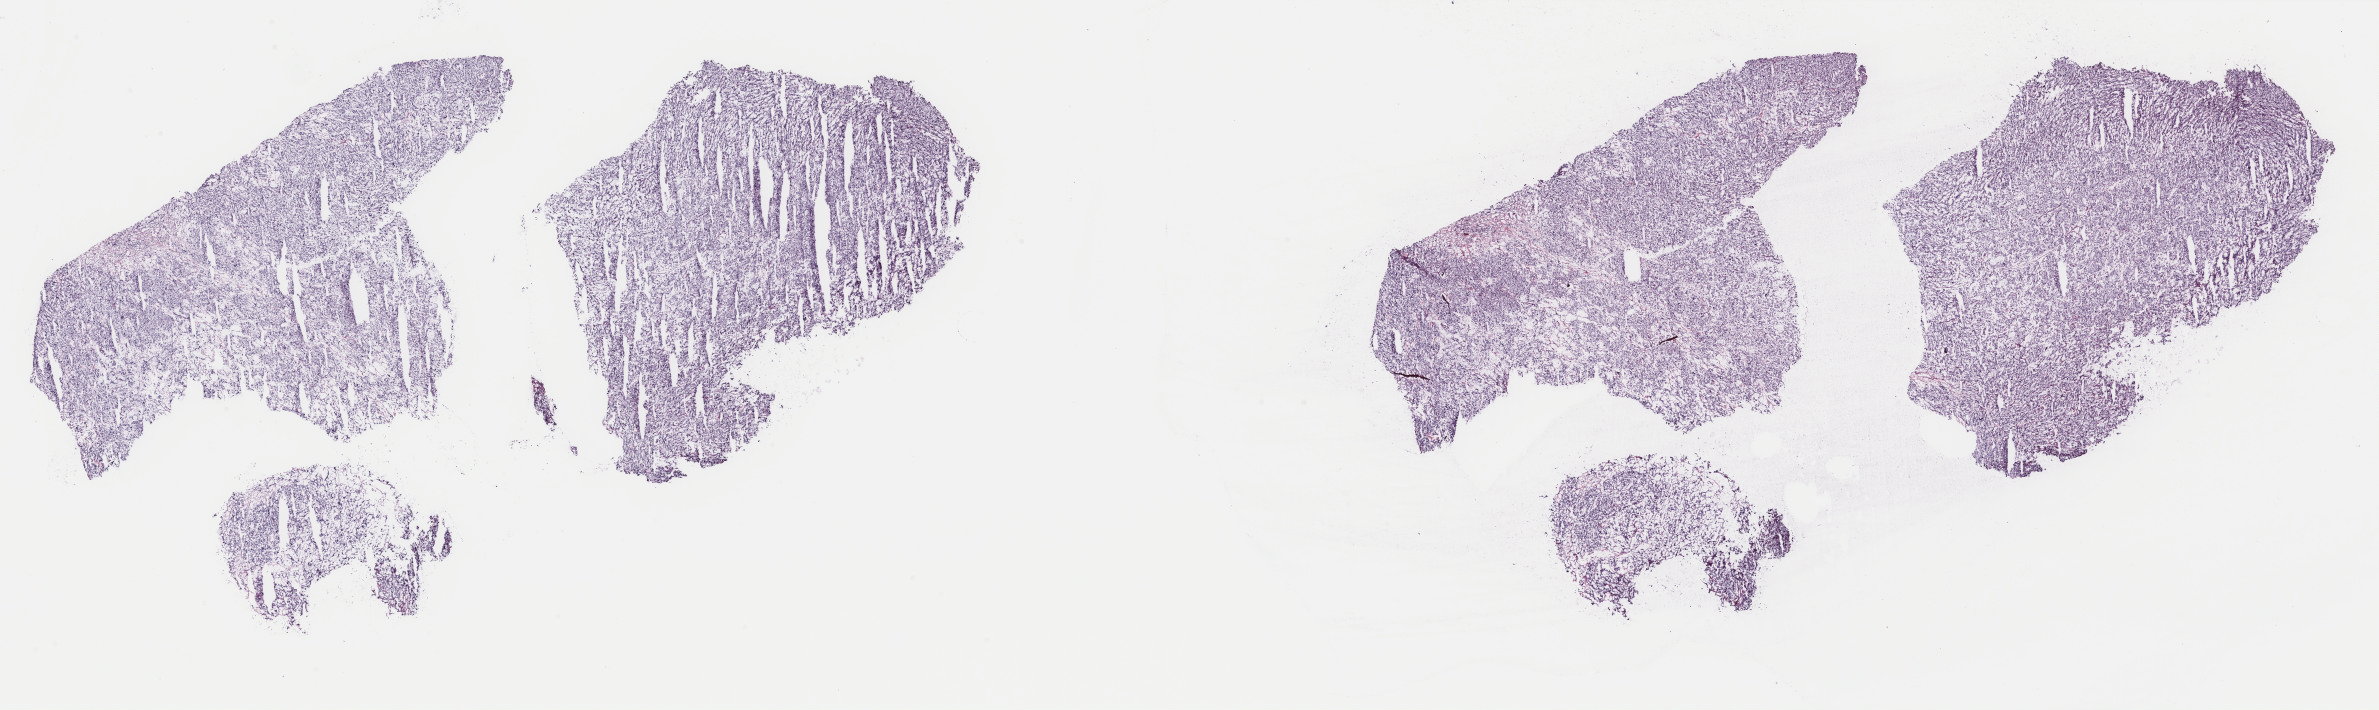
Hematoxylin and eosin (H&E) stained whole-slide image, low-resolution overview of the scanned area, about 37.8 x 11.3 mm; frozen section; adrenal gland, primary tumour sample. Male, age 31 years at initial diagnosis. Composition of this section per pathologist review: tumour cells 90%, tumour nuclei 90%, normal cells 0%, stromal cells 10%, necrosis 0%. Inflammatory infiltration, as recorded: lymphocyte infiltration 40%, monocyte infiltration 20%, neutrophil infiltration 20%.
Diagnosis: Pheochromocytoma, NOS. Laterality: right.